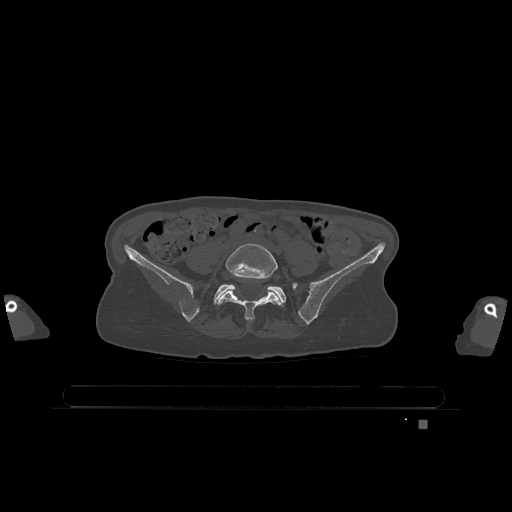
CT including the spine, one axial slice; slice 225 of 1317 in the series (ordered by position); bone window (W 1800 / L 400 HU); 512 × 512 image matrix, field of view 500 × 500 mm. Female patient, age 74 years. Case-level facts recorded for this patient, not image findings: primary cancer: lung; vertebrae with lytic lesions (as recorded): T1, T4, T5, T6, L4, L5.
Annotated regions visible in this slice (semi-automatically segmented with operator editing):
- L5 vertebra: box from (x=217, y=243) to (x=282, y=321) px